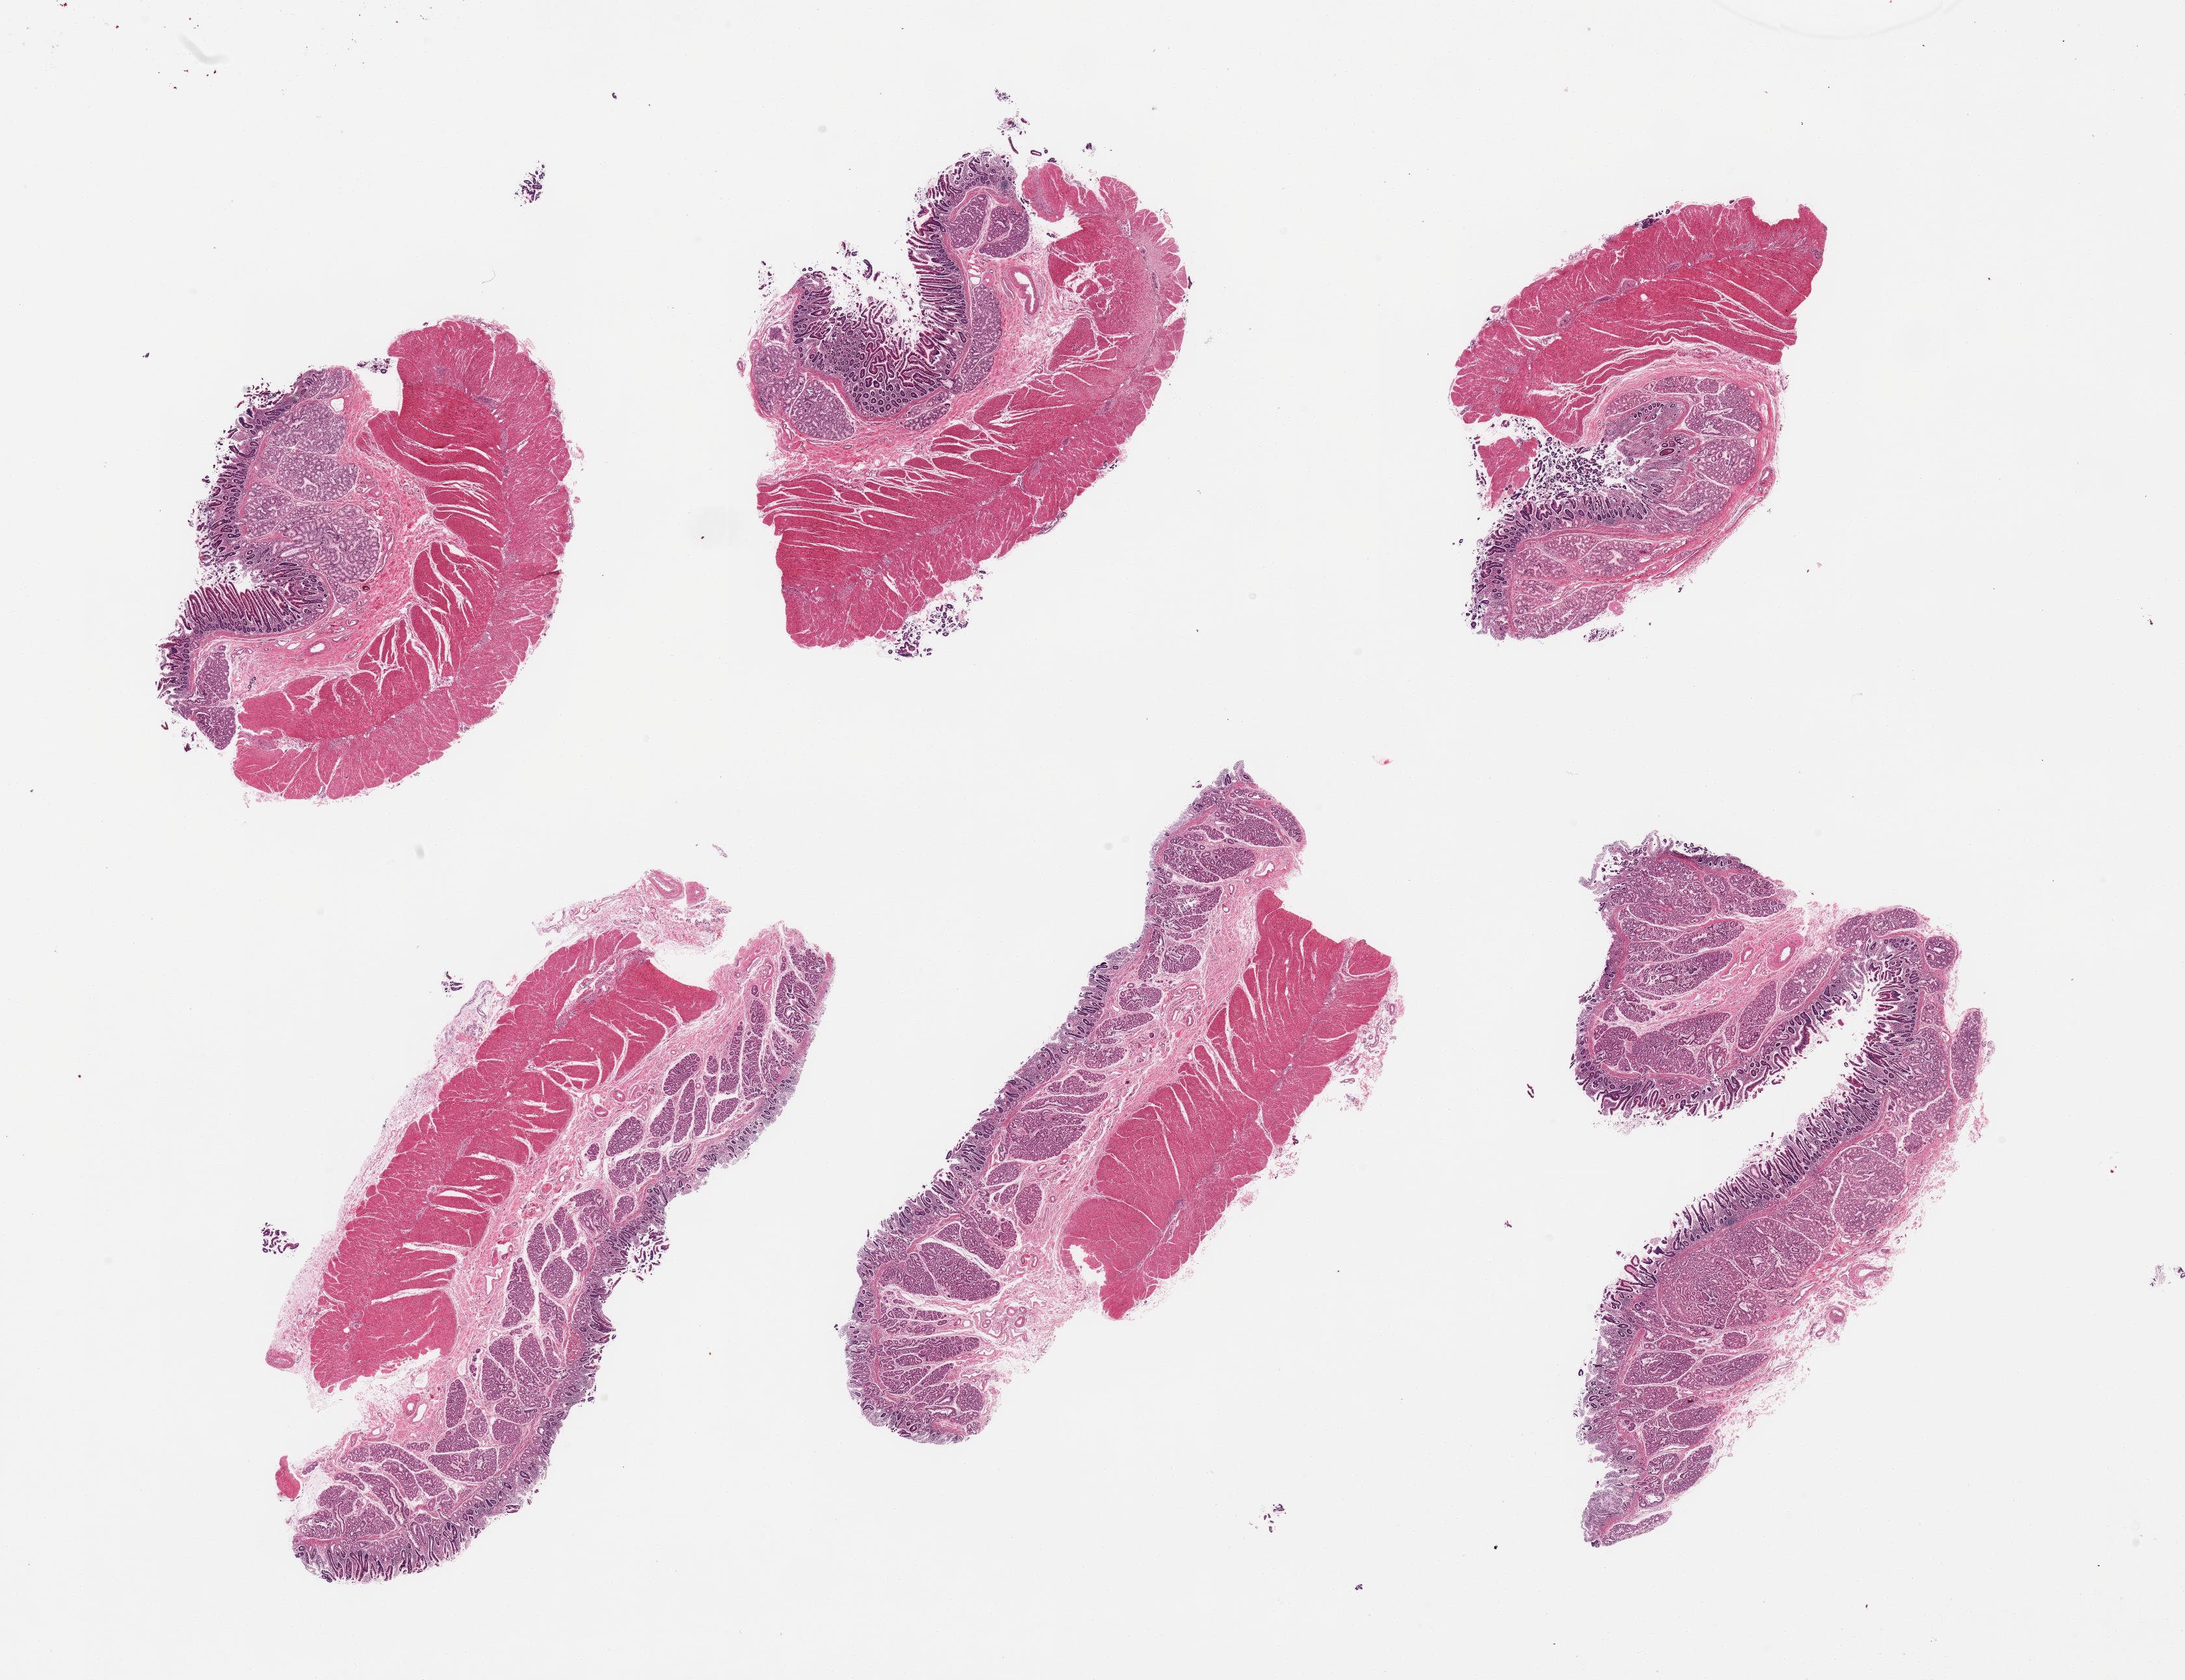
H&E whole-slide image, whole scanned area (about 26.6 x 20.4 mm, acquisition: 20x scan) shown as a low-resolution overview; PAXgene-fixed, paraffin-embedded tissue; target tissue: transverse colon; tissue donor sample.
• pathologist's review note for this sample: 6 pieces; duodenum not colon